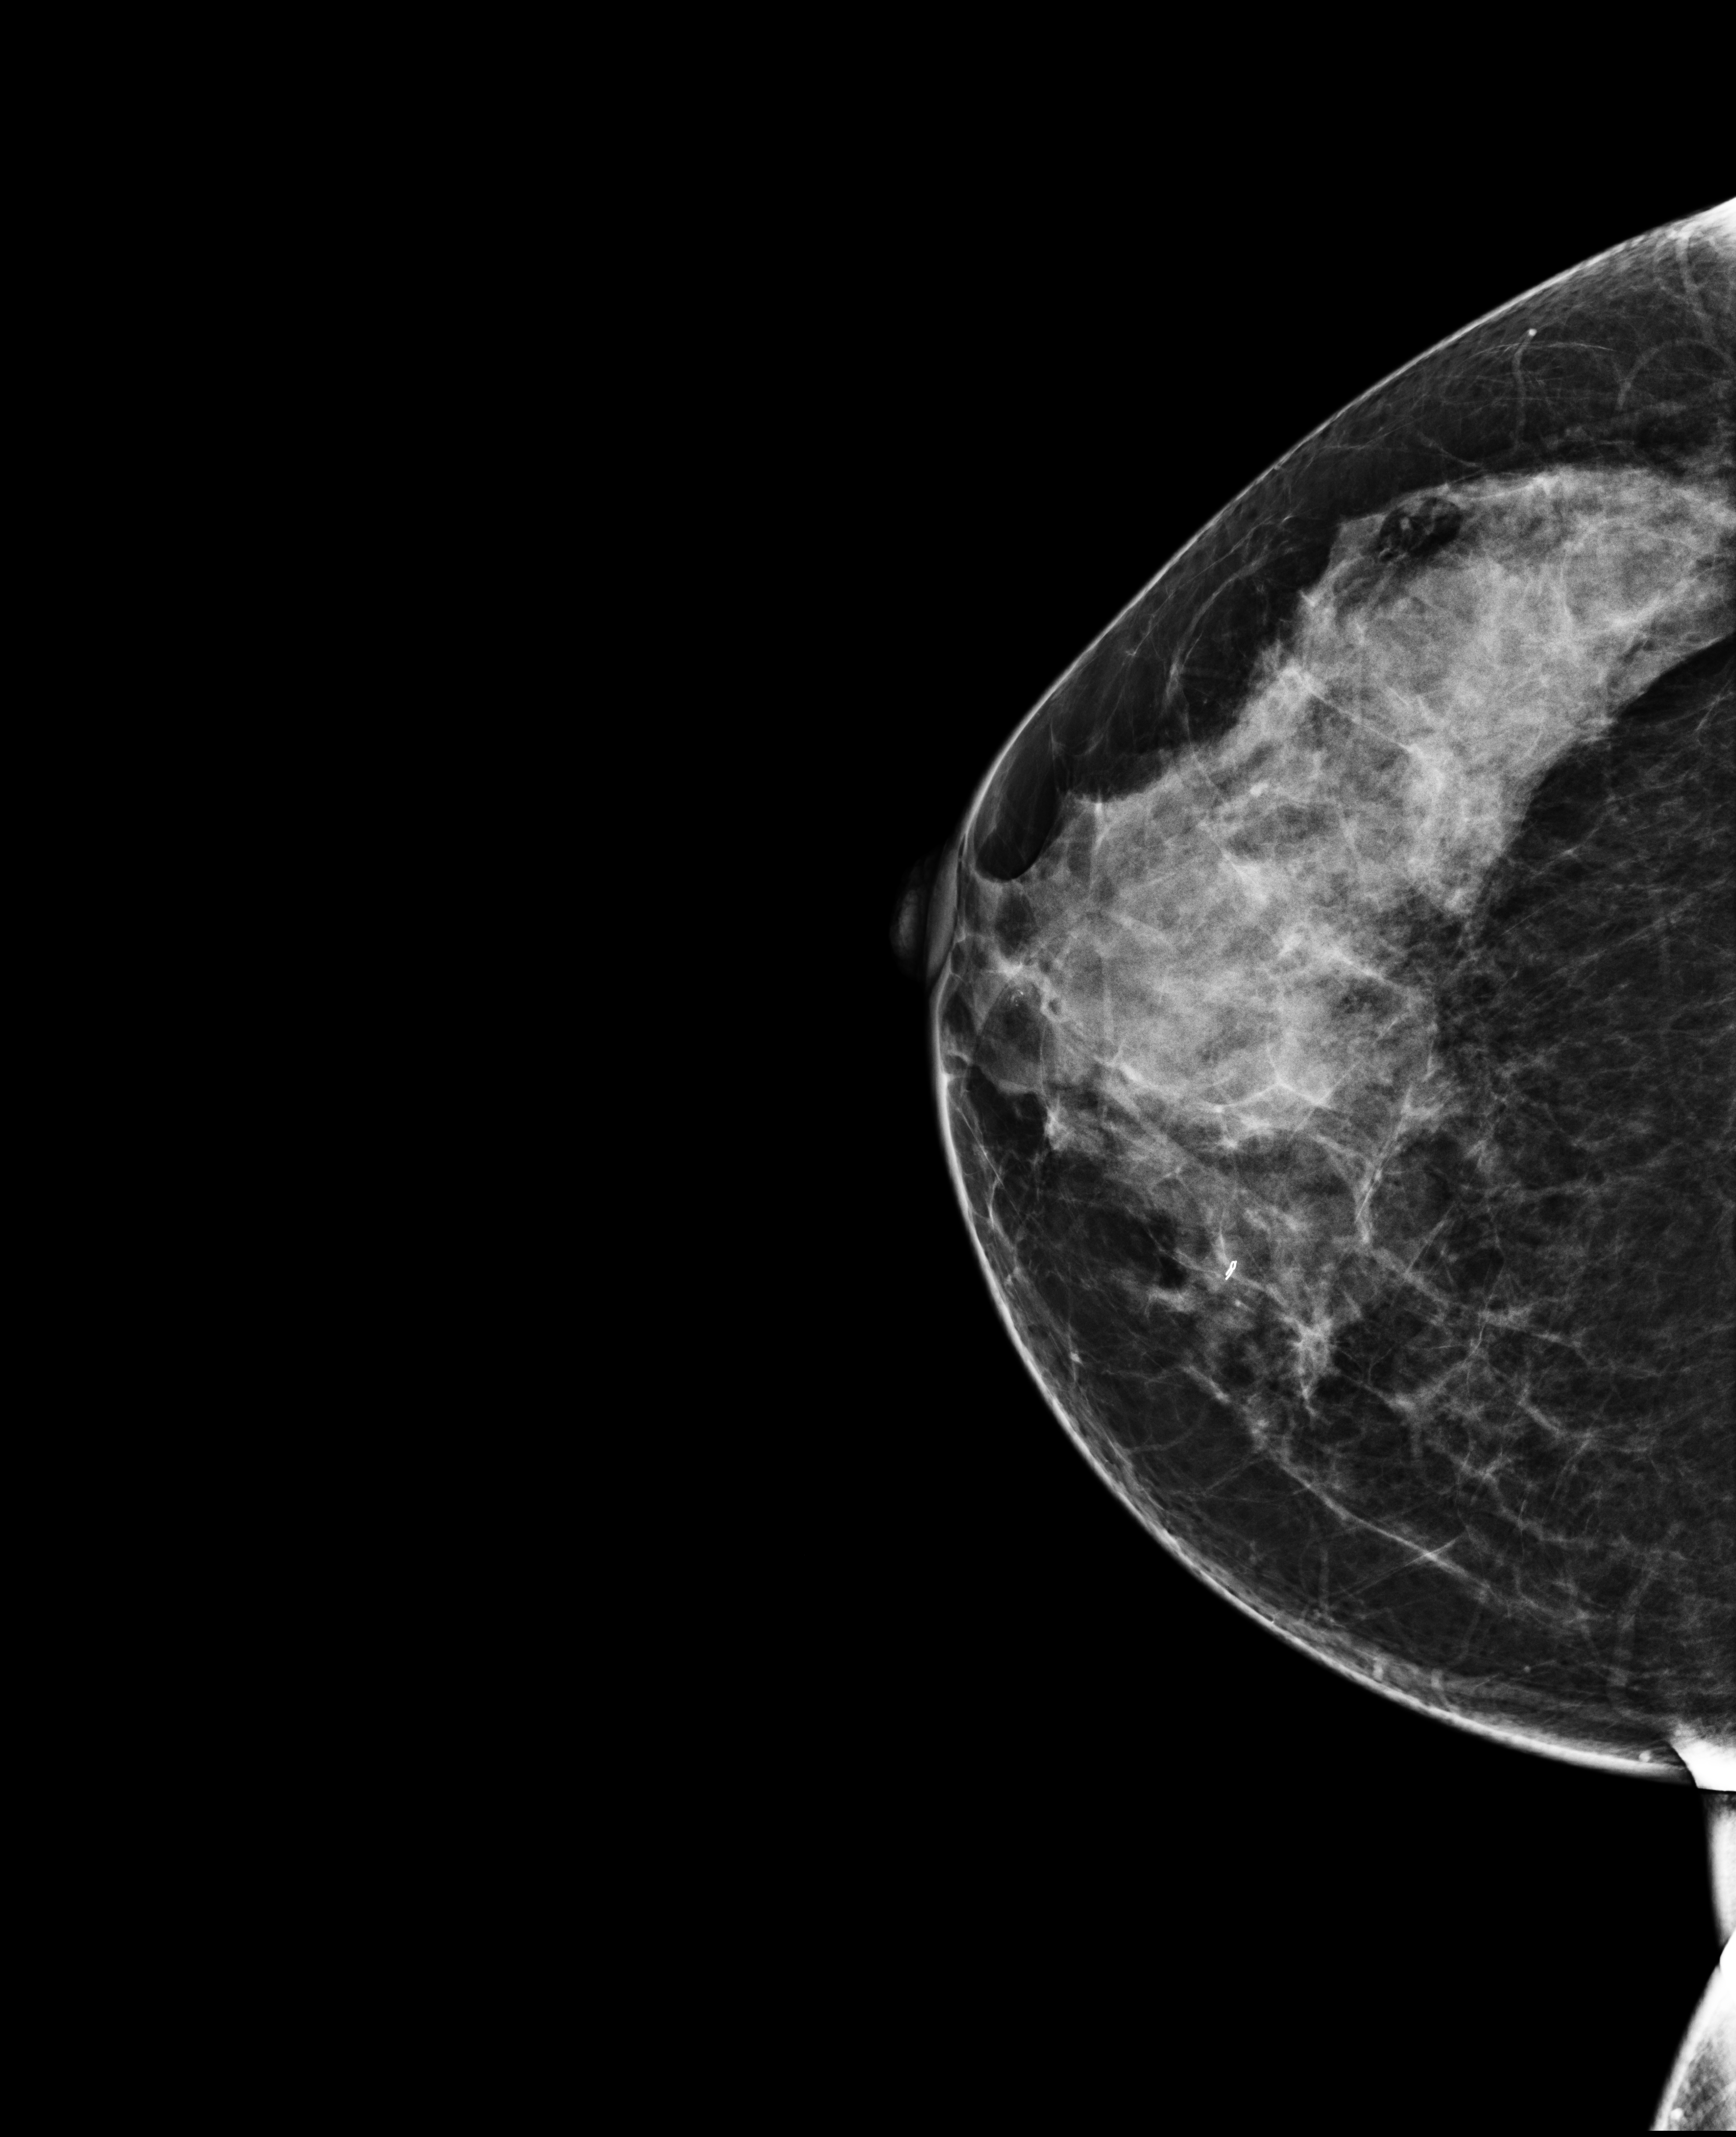
Digital mammogram (FFDM), right breast, CC view, screening examination. Female patient, age 46 years.
BI-RADS breast density category at the screening exam (both breasts, scale 1–4): 3. Final BI-RADS category for the screening round (tomosynthesis exam, both breasts): category 5. Recall: no recall after this screen.